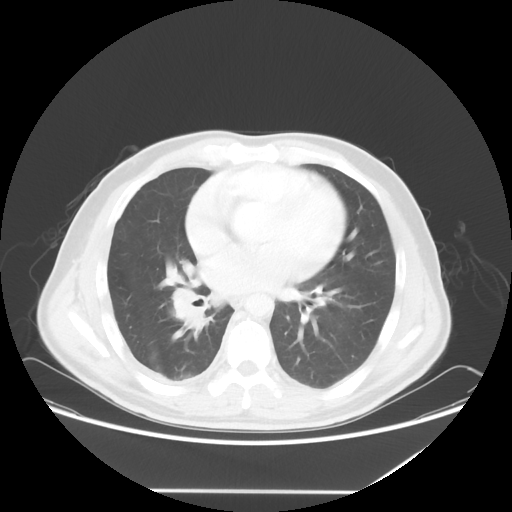
Chest CT, one axial slice. Slice 28 of 60 in the series (ordered by position). 120 kVp. Lung window (W 1500 / L -600 HU). 512 × 512 image matrix. Patient: male, 48 years. Case-level facts recorded for this patient, not image findings: clinical TNM (as recorded): T3 N3 M1a.
Outlined on this slice (rectangle marked by the reading radiologist):
- lung tumour (recorded histology: squamous cell carcinoma): bounding box <168,282,216,342> (left, top, right, bottom; pixels)